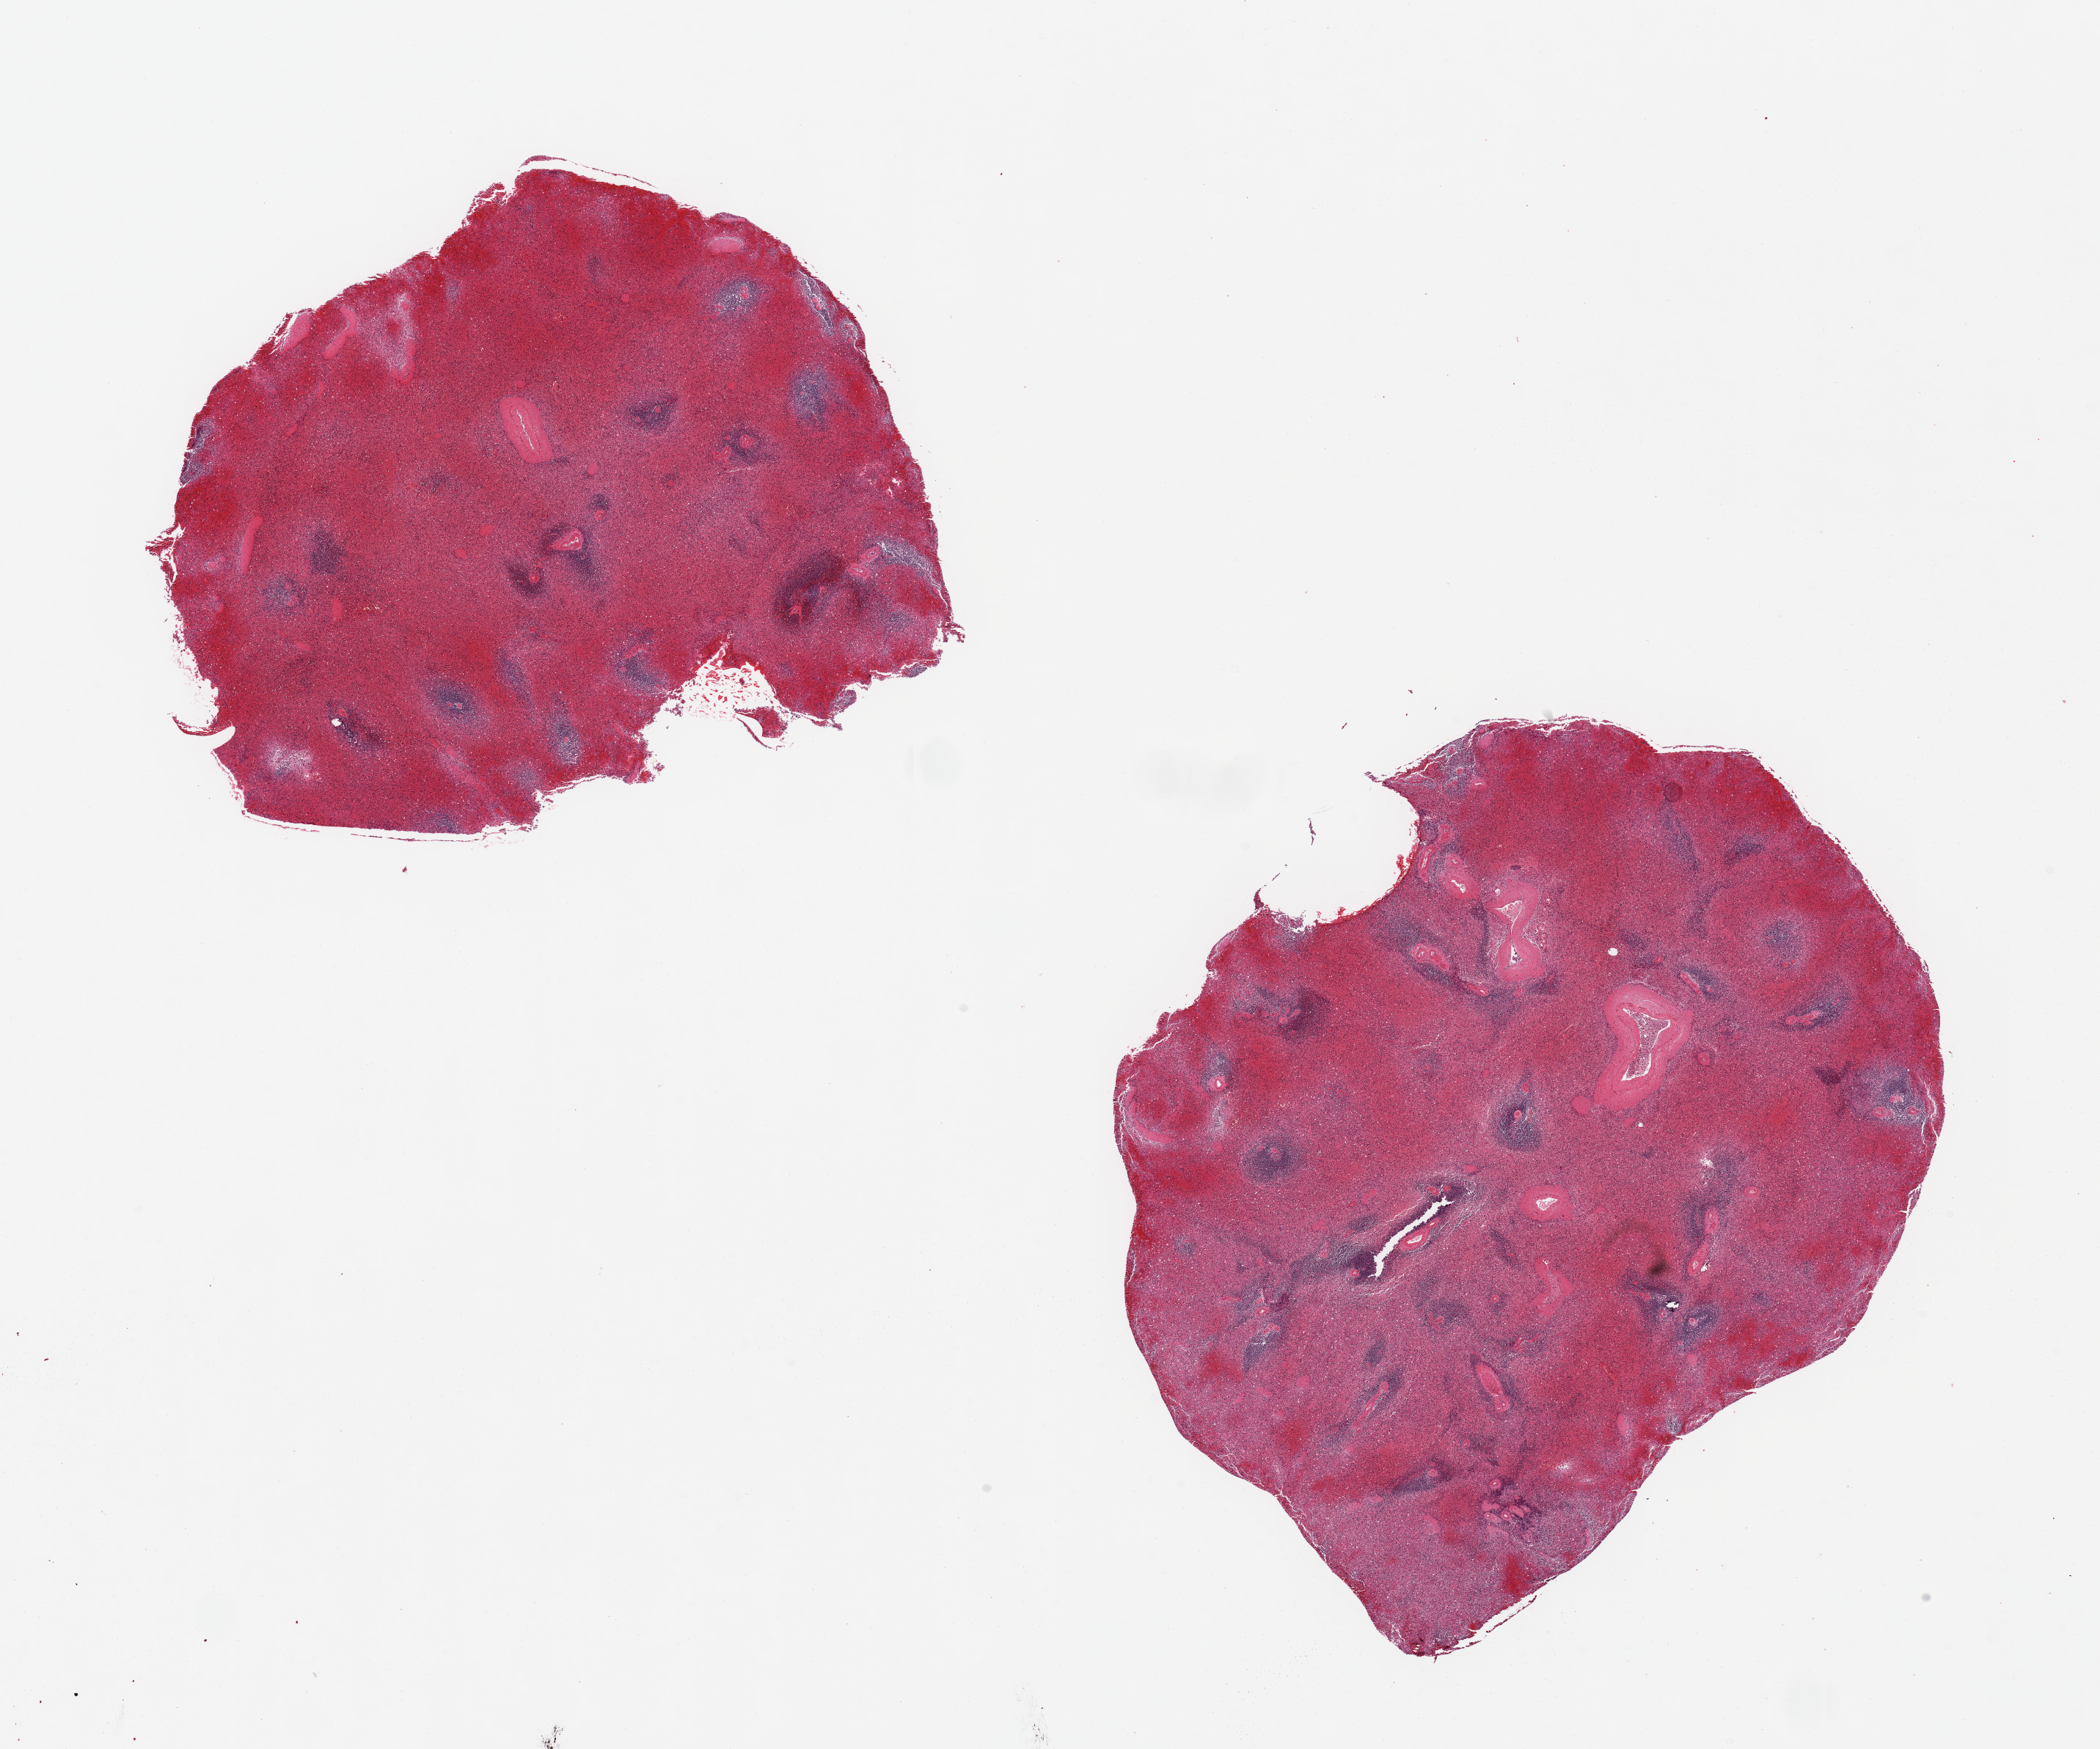
Whole-slide image, hematoxylin and eosin (H&E) stain — low-resolution overview of the scanned area, about 22.6 x 18.9 mm (slide scanned at 20x); PAXgene-fixed paraffin-embedded (PFPE) section; target tissue: spleen; donor tissue sample. Donor sex: male.
Pathologist's review note for this sample: 2 pieces ~8x7mm, markedly congested, badly autolyzed.